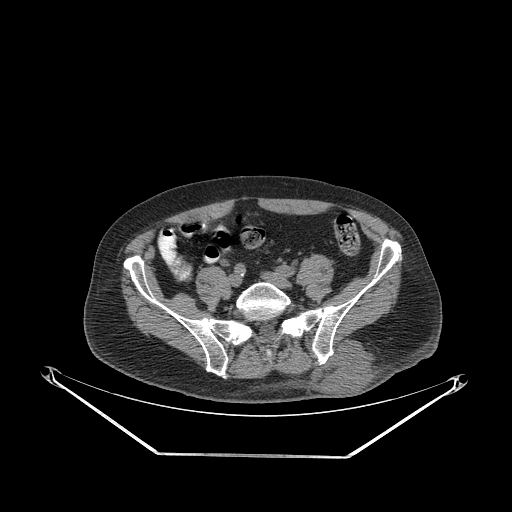
CT of an extremity soft-tissue mass (from a PET/CT study), one axial slice; position 82 of 267 along the scan axis; reconstruction kernel STANDARD; soft-tissue window (W 400 / L 40 HU); 512 × 512 image matrix, field of view 500 × 500 mm. Male patient. From the clinical record (not read from this slice): histological type: leiomyosarcoma; grade: intermediate; site of the primary tumour: left pelvis.
Outlined on this slice (expert contour drawn on MRI and transferred to this co-registered scan by the dataset authors):
- gross tumour volume (mass): box from (x=311, y=340) to (x=378, y=396) px